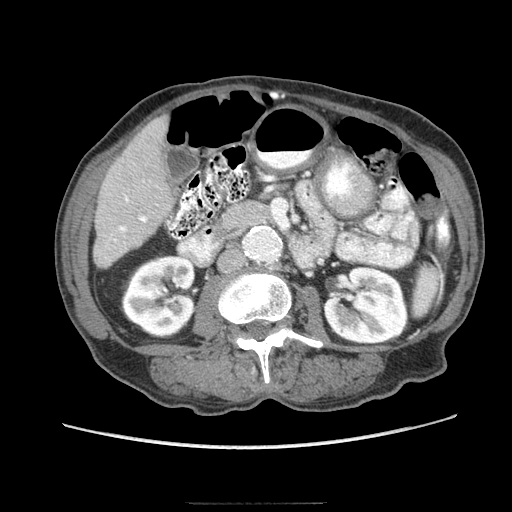
Contrast-enhanced abdominal CT (liver protocol), one axial slice. Slice 25 of 83 in the series (ordered by position). Reconstruction kernel STANDARD. Soft-tissue window (W 400 / L 40 HU). 2.5 mm slice thickness. 512 × 512 image matrix, field of view 360 × 360 mm. Case-level facts recorded for this patient, not image findings: diagnosis: hepatocellular carcinoma (patient treated with transarterial chemoembolisation; whether this scan precedes or follows treatment is not stated here); TNM stage (as recorded): Stage-I; Child-Pugh class: A; tumour nodularity: uninodular.
Annotated regions visible in this slice (semi-automatic segmentation, software-assisted and operator-edited):
- liver parenchyma outside the tumour (the mass and vessels are separate outlines, so this box may not span the whole liver): bounding box <94,116,174,268> (left, top, right, bottom; pixels)
- liver vessels: <114,196,147,241>